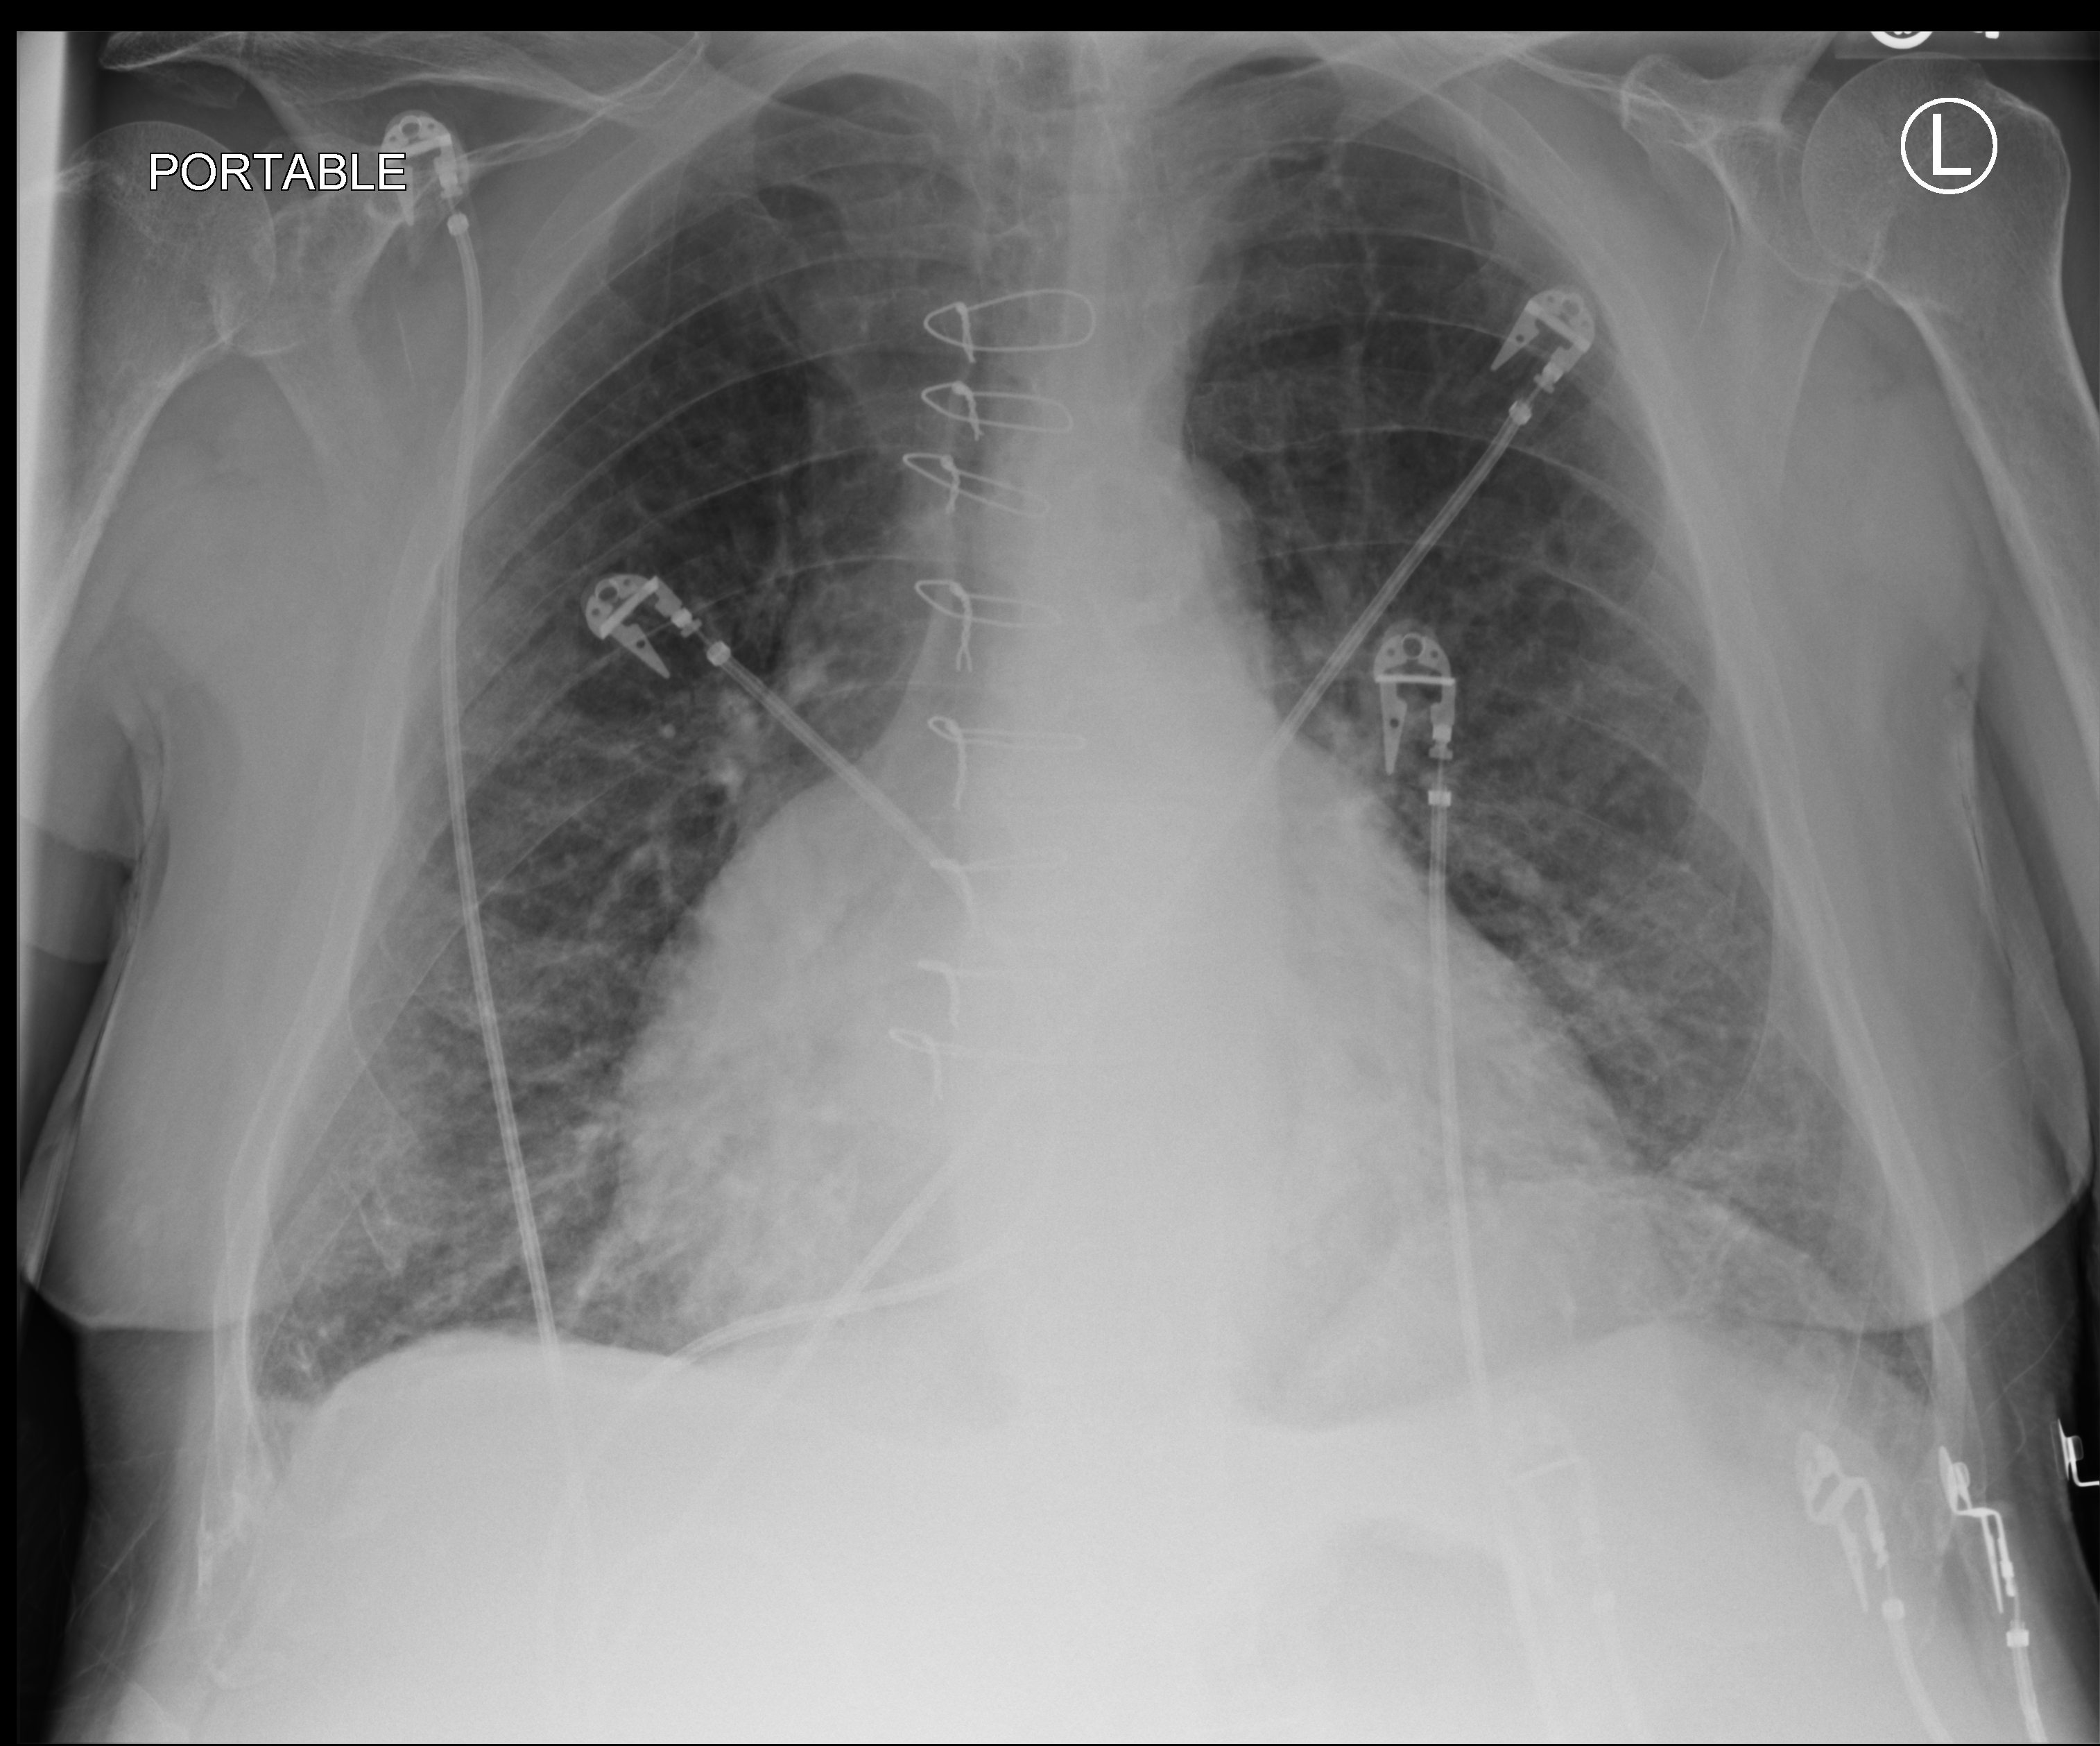
Portable chest radiograph; anteroposterior (AP) projection. Male patient hospitalised with COVID-19, age 75–90 years.
Hospital-stay facts (about this admission, not read from this image; timing relative to this image not recorded): admitted to intensive care during this hospital stay: yes; mechanically ventilated during this hospital stay: yes; length of hospital stay: 40 days.